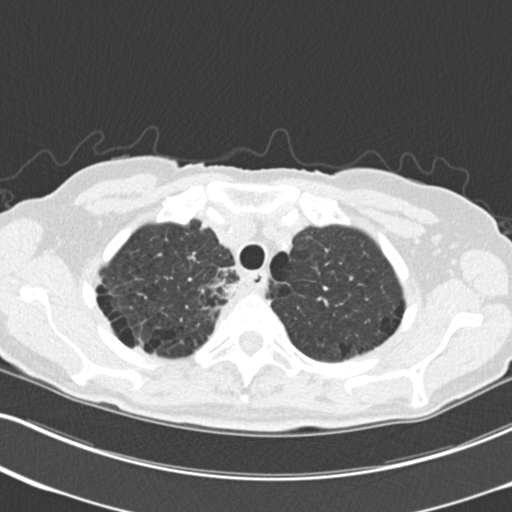
Low-dose screening chest CT, one axial slice. Position 186 of 226 along the scan axis. 120 kVp. Lung window (W 1500 / L -600 HU). 2 mm slice thickness. 512 × 512 image matrix, field of view 322 × 322 mm.
Outlined on this slice (expert manual segmentation):
- lesion 1 (tumor, mediastinum): bounding box <201,279,239,300> (left, top, right, bottom; pixels)